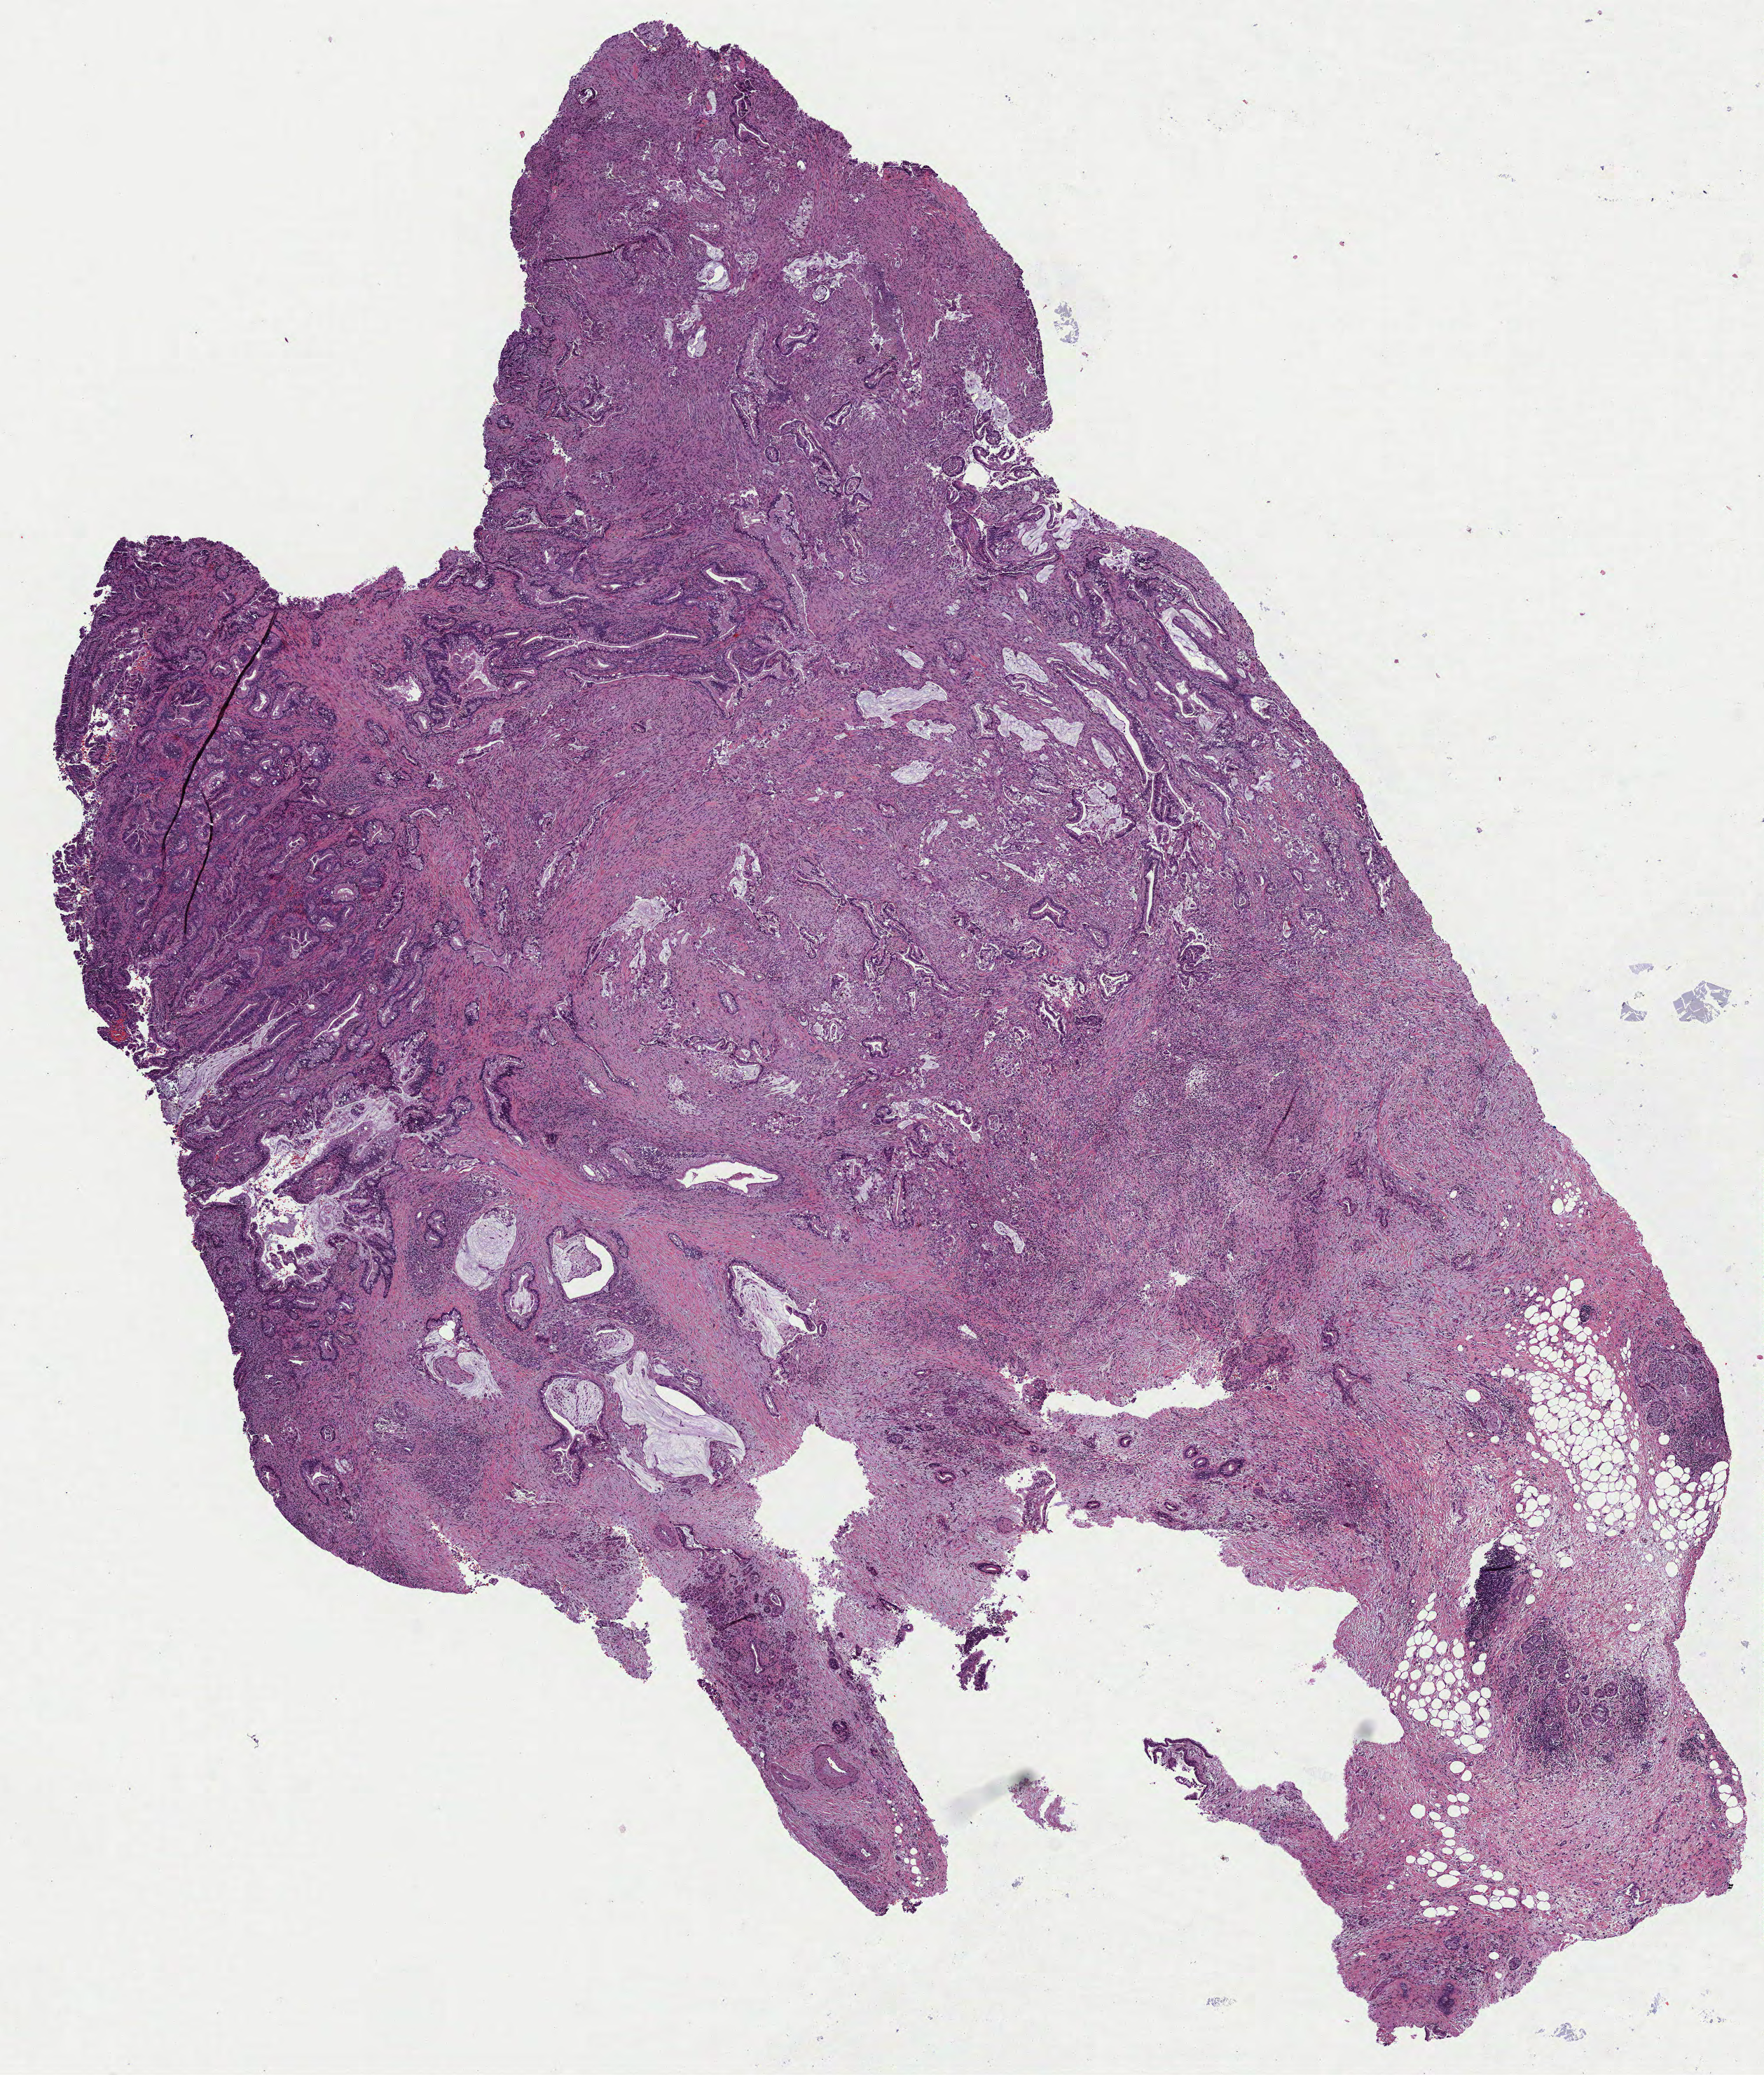
Digitized H&E tissue section (whole slide), low-resolution overview of the scanned area, about 10.2 x 11.9 mm (from a 40x scan); formalin-fixed paraffin-embedded (FFPE) diagnostic section; sample: primary tumour, pancreas. Male, age 77 years at initial diagnosis. Histologic grade: G1 (well differentiated).
• diagnosis: Adenocarcinoma, NOS (head of pancreas)
• lymph nodes positive (case pathology): 1 of 21 examined
• TNM: T3 N1 MX
• AJCC pathologic stage: IIB (7th edition)